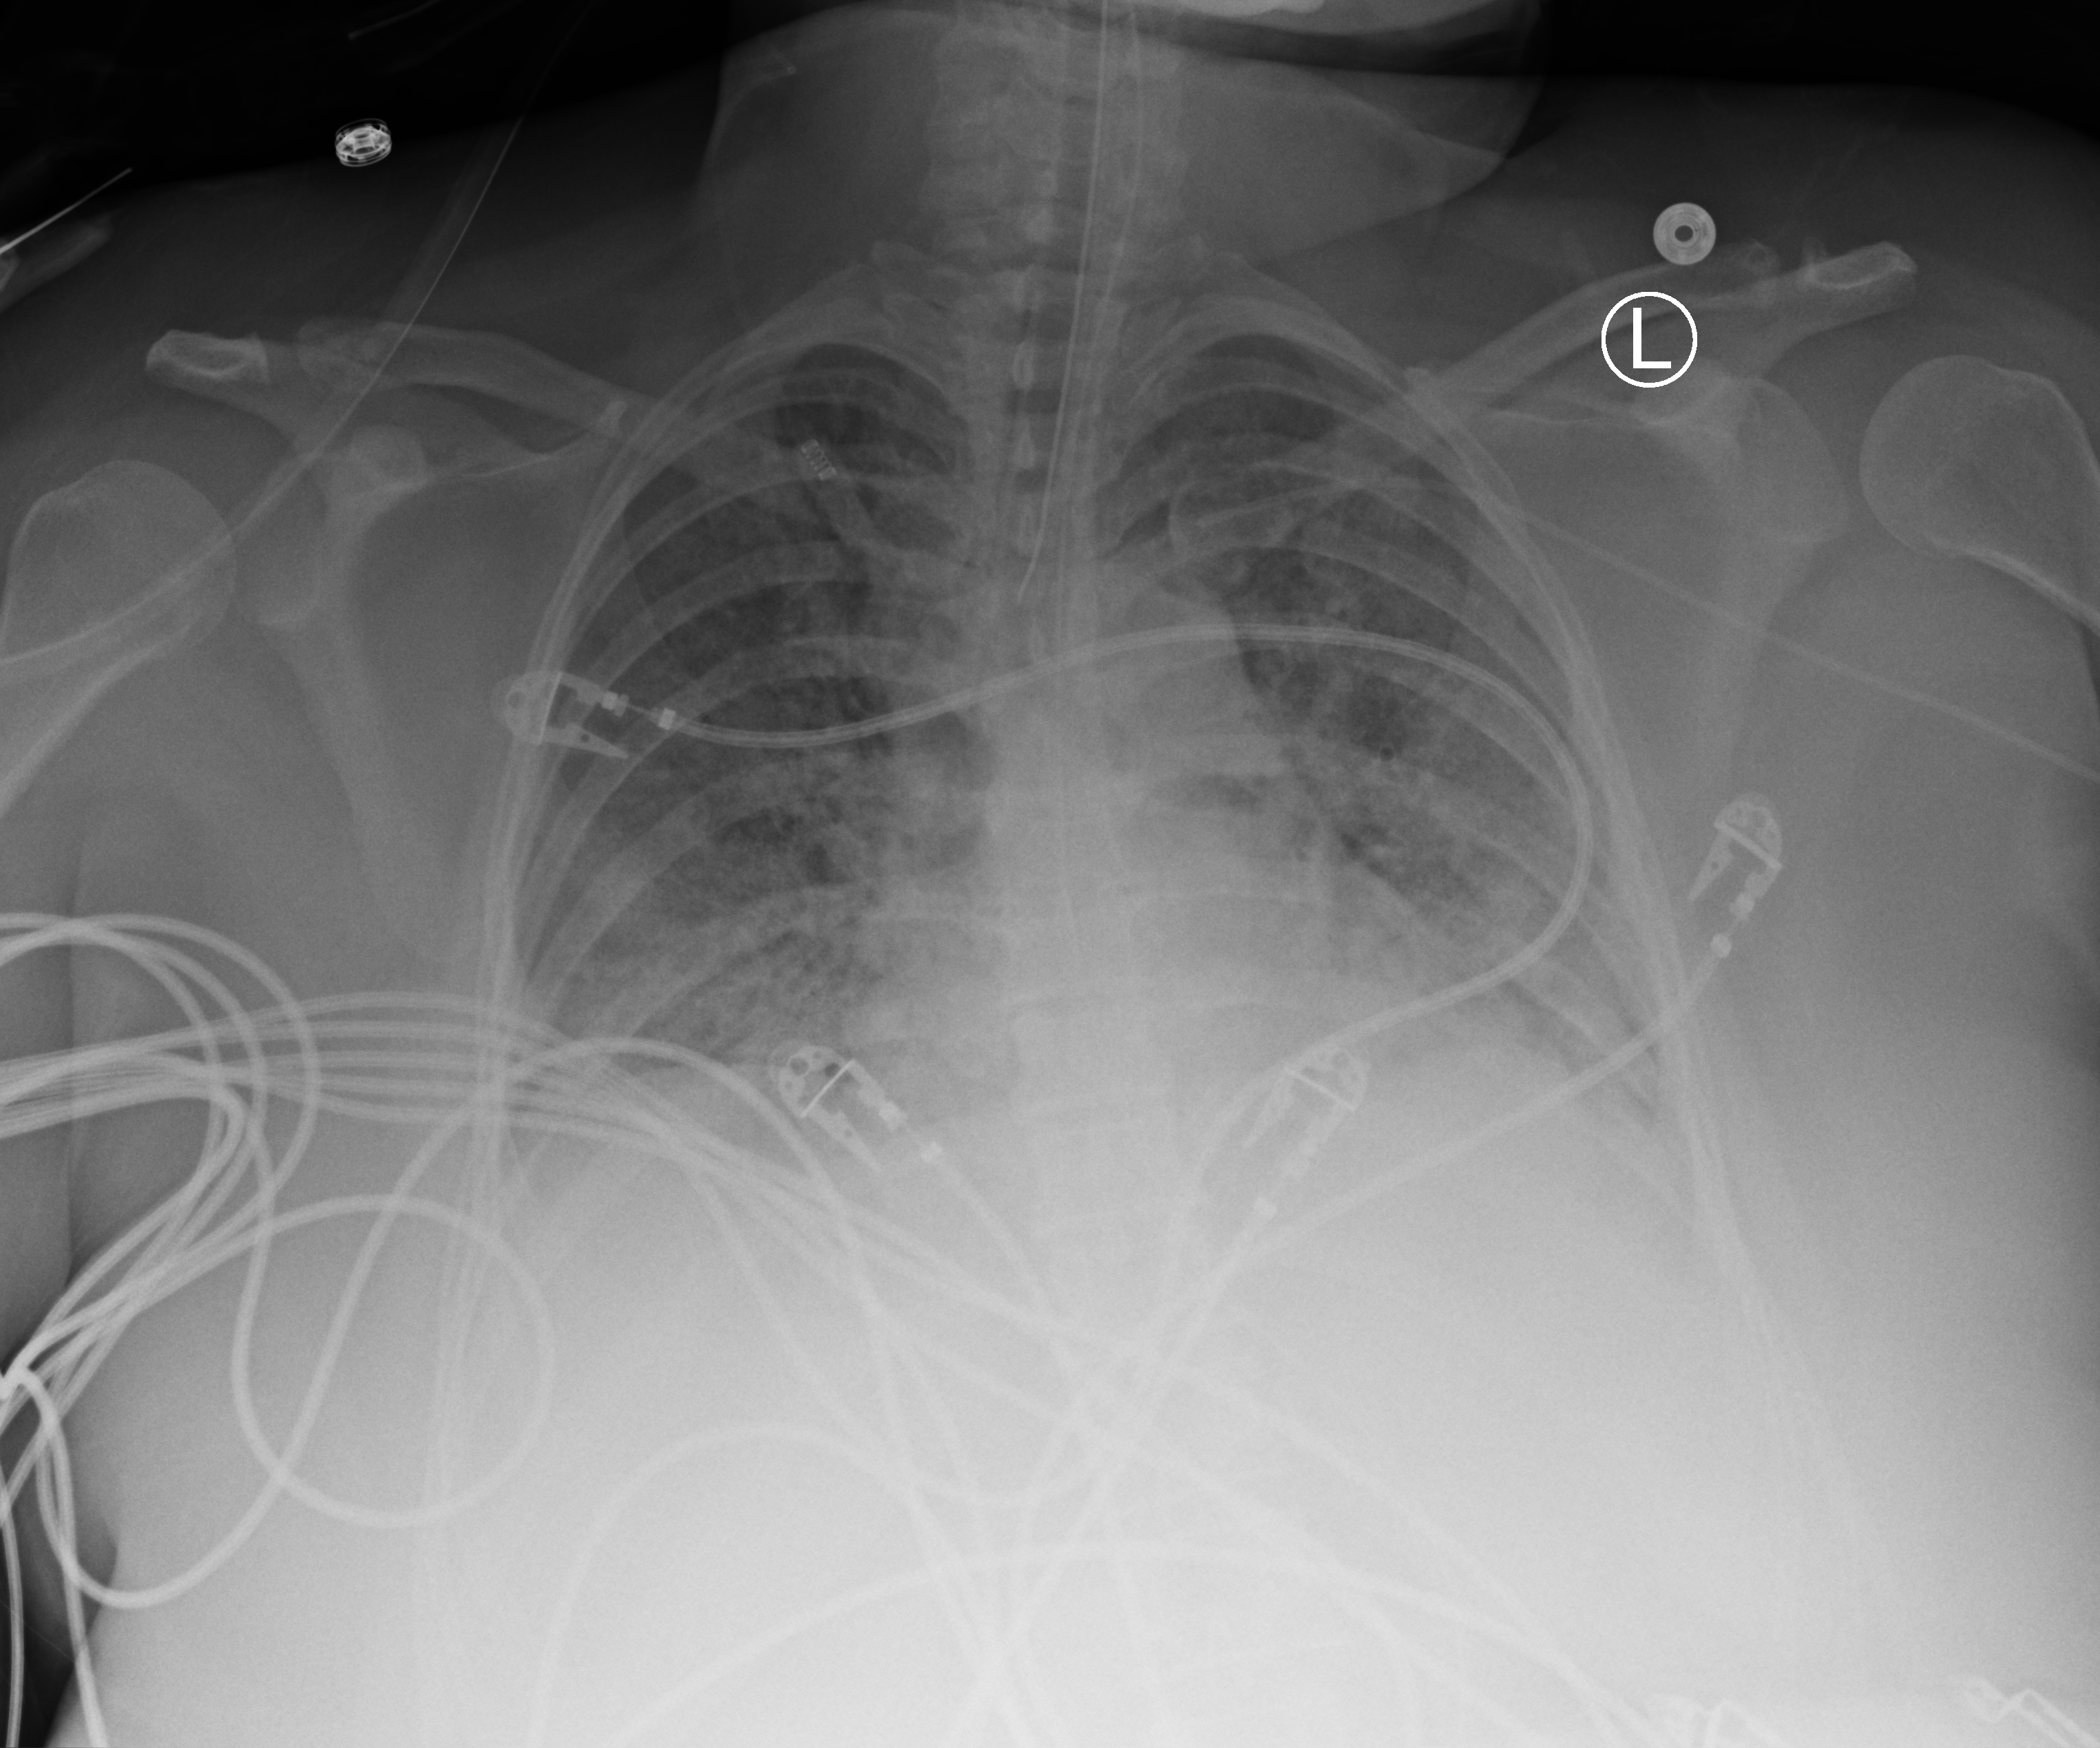
Portable chest radiograph. Female patient hospitalised with COVID-19, age 18–59 years.
From the hospital-stay record, not from the radiograph (when in the stay this image was taken is not recorded): chronic kidney disease (admission record): no.